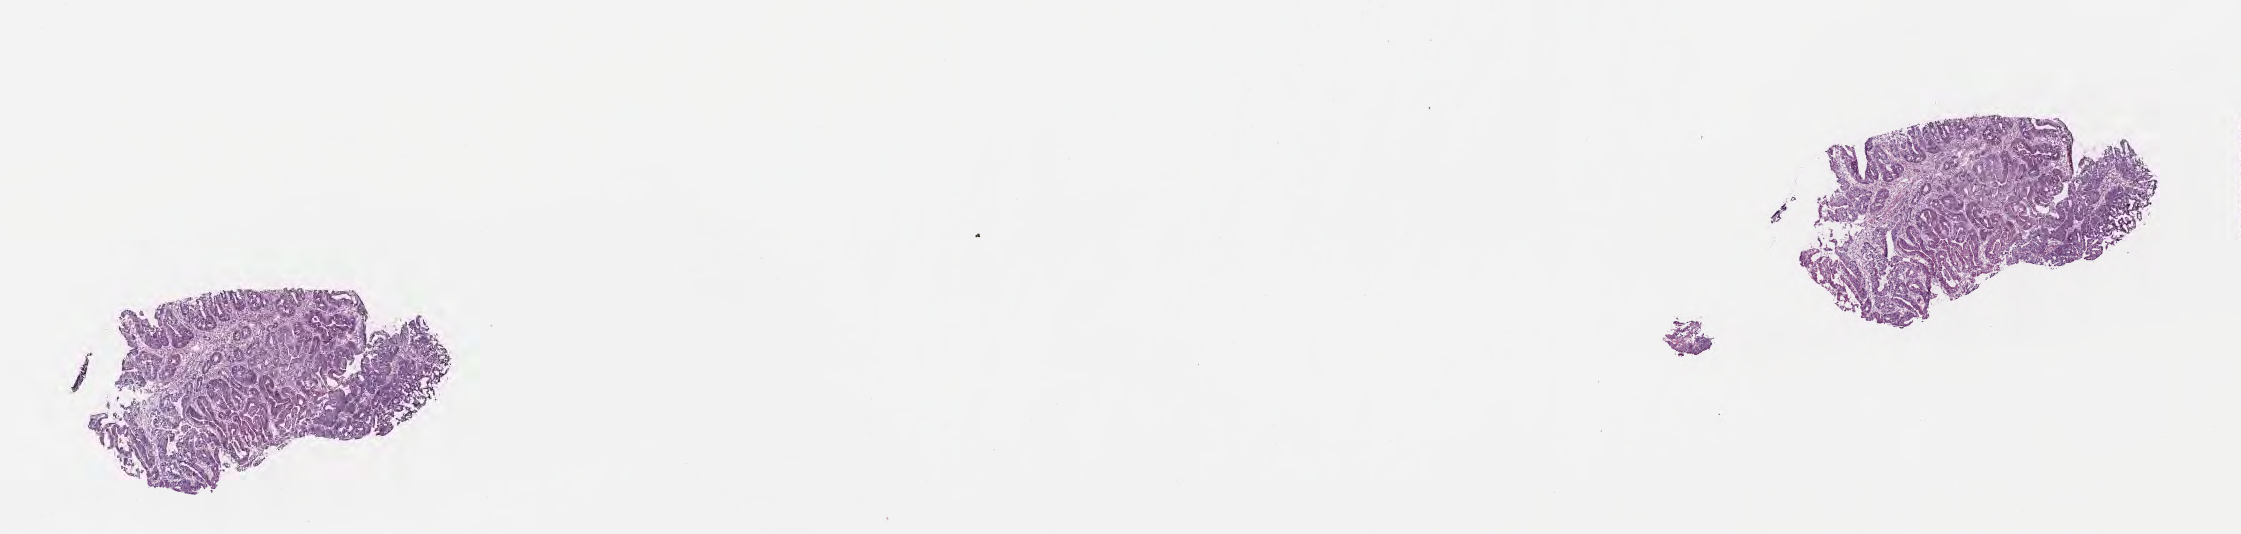
Haematoxylin and eosin whole-slide image — low-resolution overview of the scanned area, about 18.1 x 4.3 mm; frozen section; specimen: primary tumor; anatomic site: rectosigmoid junction. Female patient; age at initial diagnosis 70 years. Tumor grade: G2 (moderately differentiated). Slide review estimates, as recorded: tumor cells 75%, tumor nuclei 75%, stromal cells 25%, necrosis 0%, normal cells 0%. Inflammatory infiltration, as recorded: lymphocyte infiltration 6%, monocyte infiltration 2%, neutrophil infiltration 7%.
Histologic diagnosis: Adenocarcinoma, NOS. AJCC pathologic stage: Stage I. Section: bottom of the tissue portion.